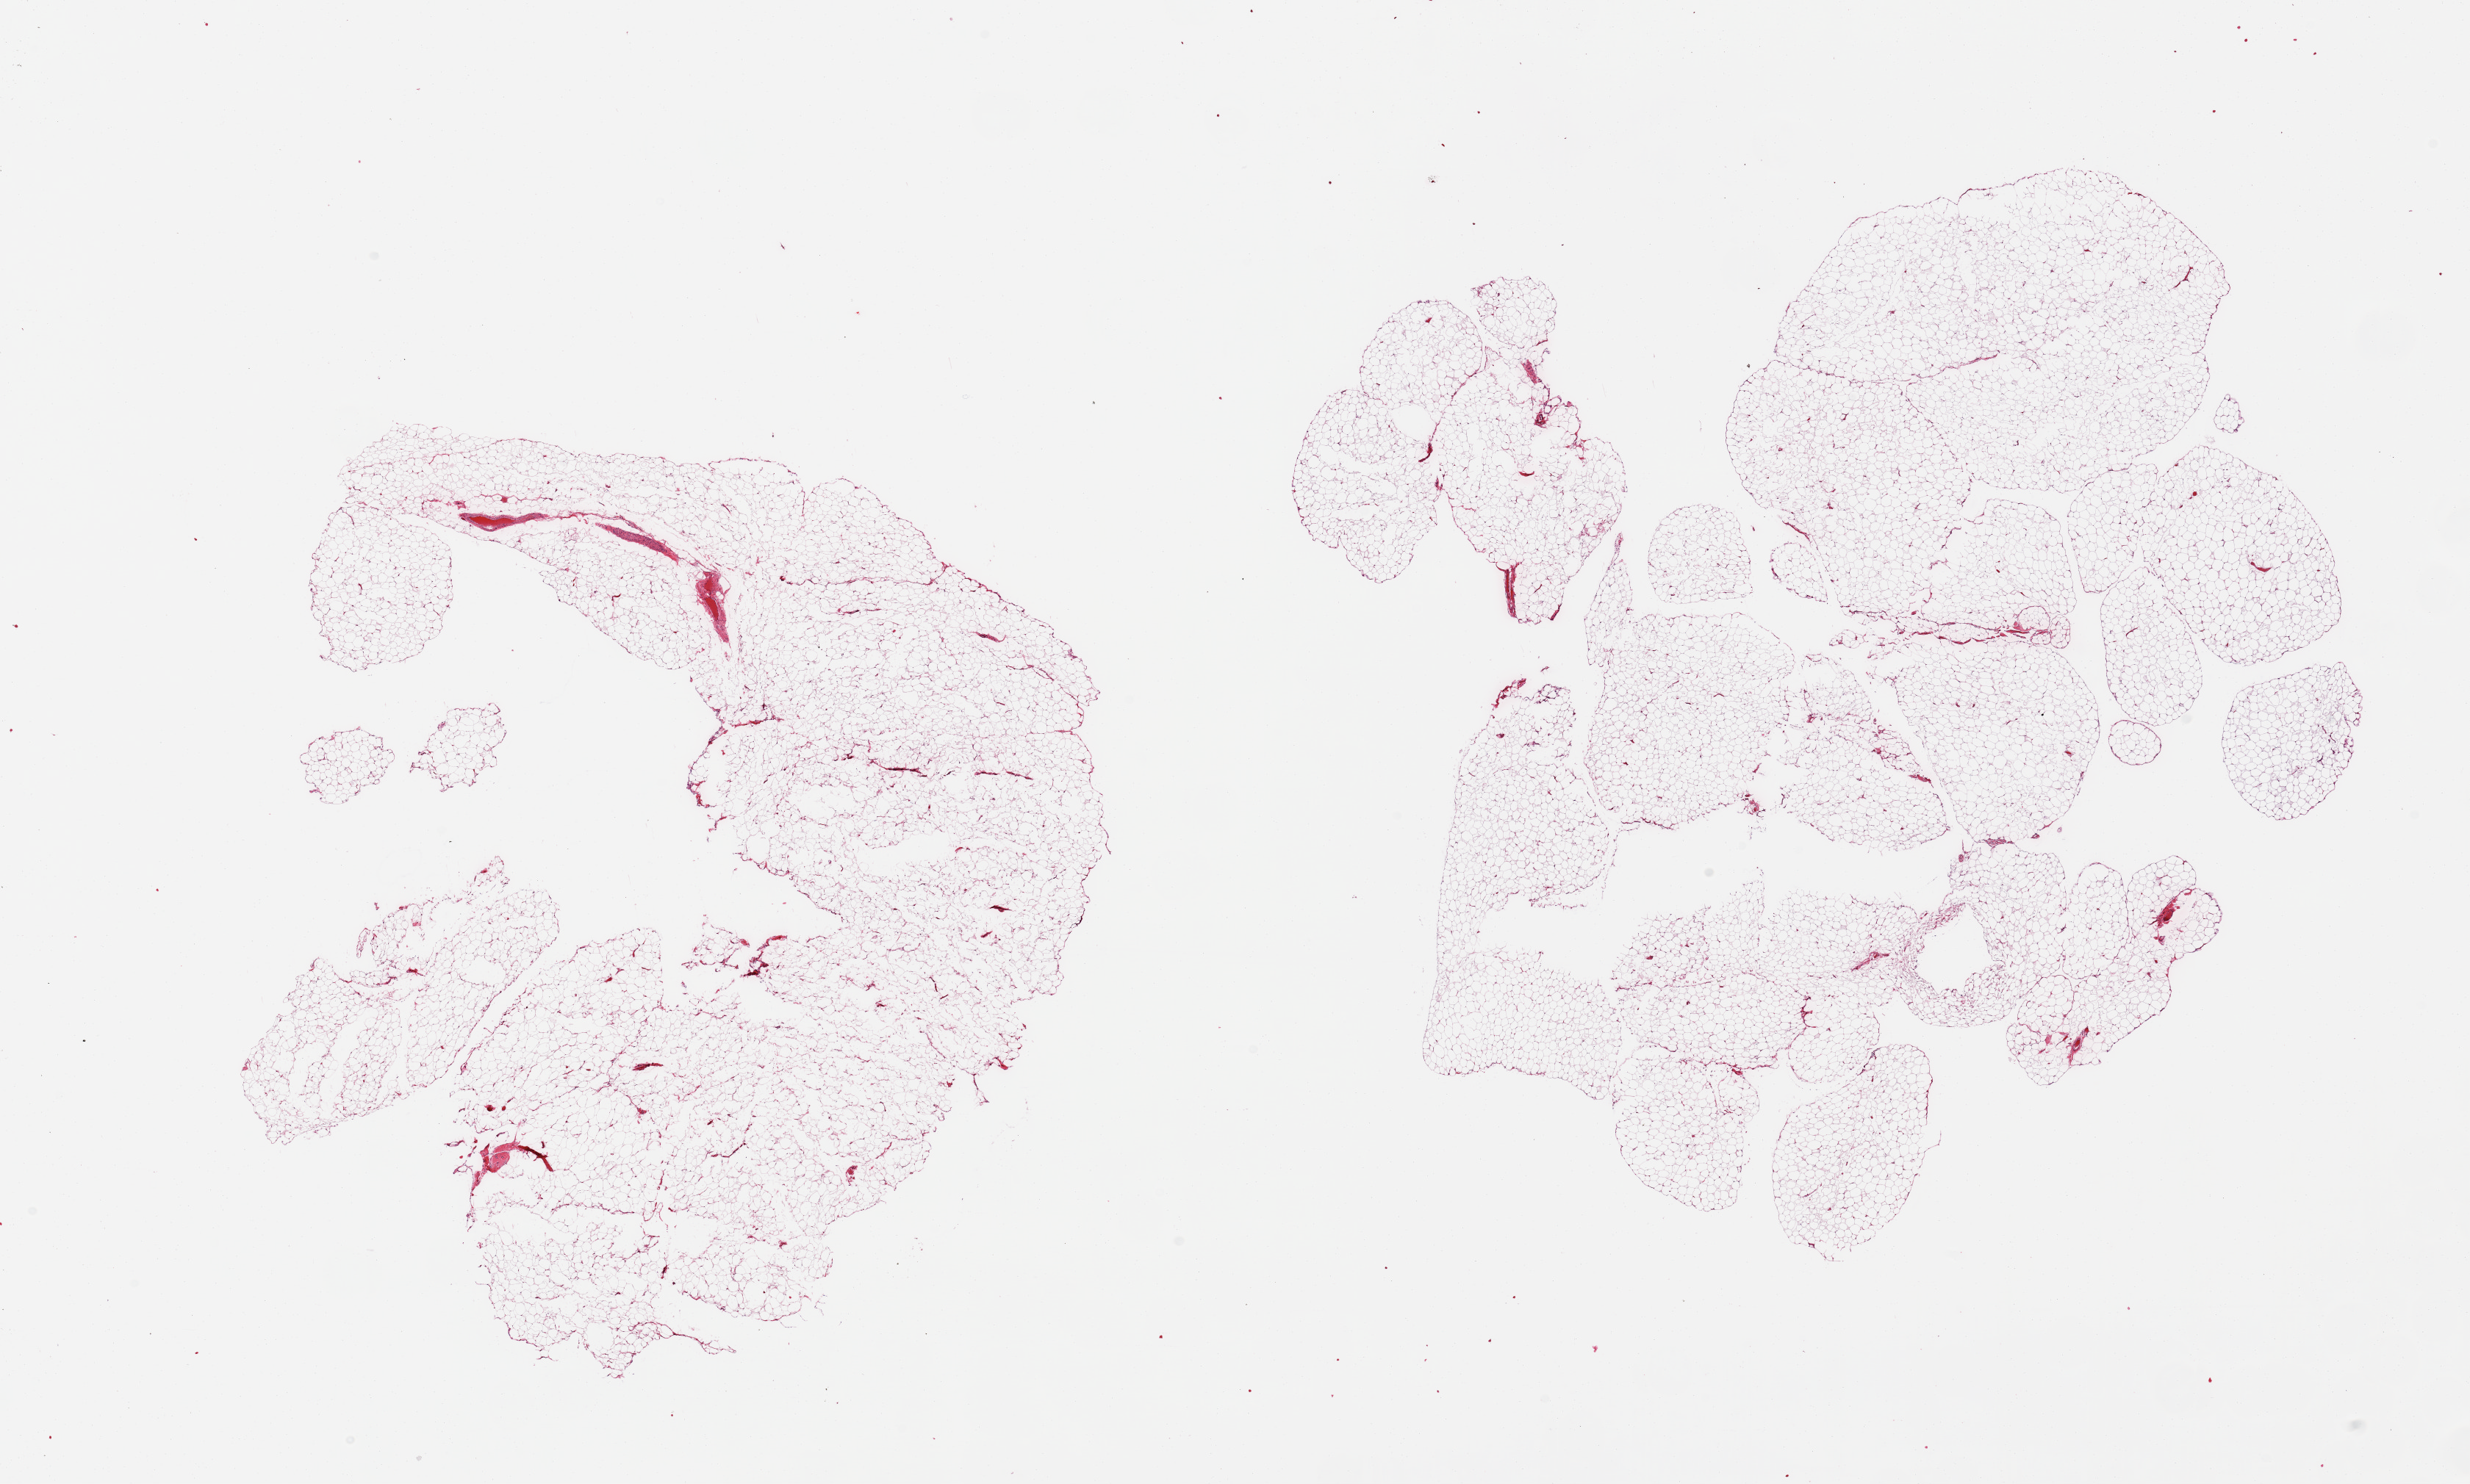
Whole-slide image, hematoxylin and eosin (H&E) stain, whole scanned area (about 26.6 x 16.0 mm) shown as a low-resolution overview, PAXgene-fixed paraffin-embedded (PFPE) section, target tissue: omentum, tissue donor sample.
- review note (as recorded): 2 pieces; mature adipose tissue